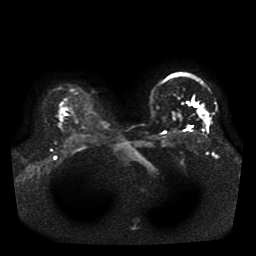
Breast MRI, one axial slice. Position 31 of 41 along the scan axis. Diffusion-weighted series; image 2 of 4 stored at this slice position (different b-values; order by instance number). 1.5 T. 5 mm slice thickness. 256 × 256 image matrix, field of view 330 × 330 mm. Female patient.
Annotated regions visible in this slice (expert manual segmentation):
- tumour on diffusion-weighted imaging: box from (x=202, y=115) to (x=210, y=122) px